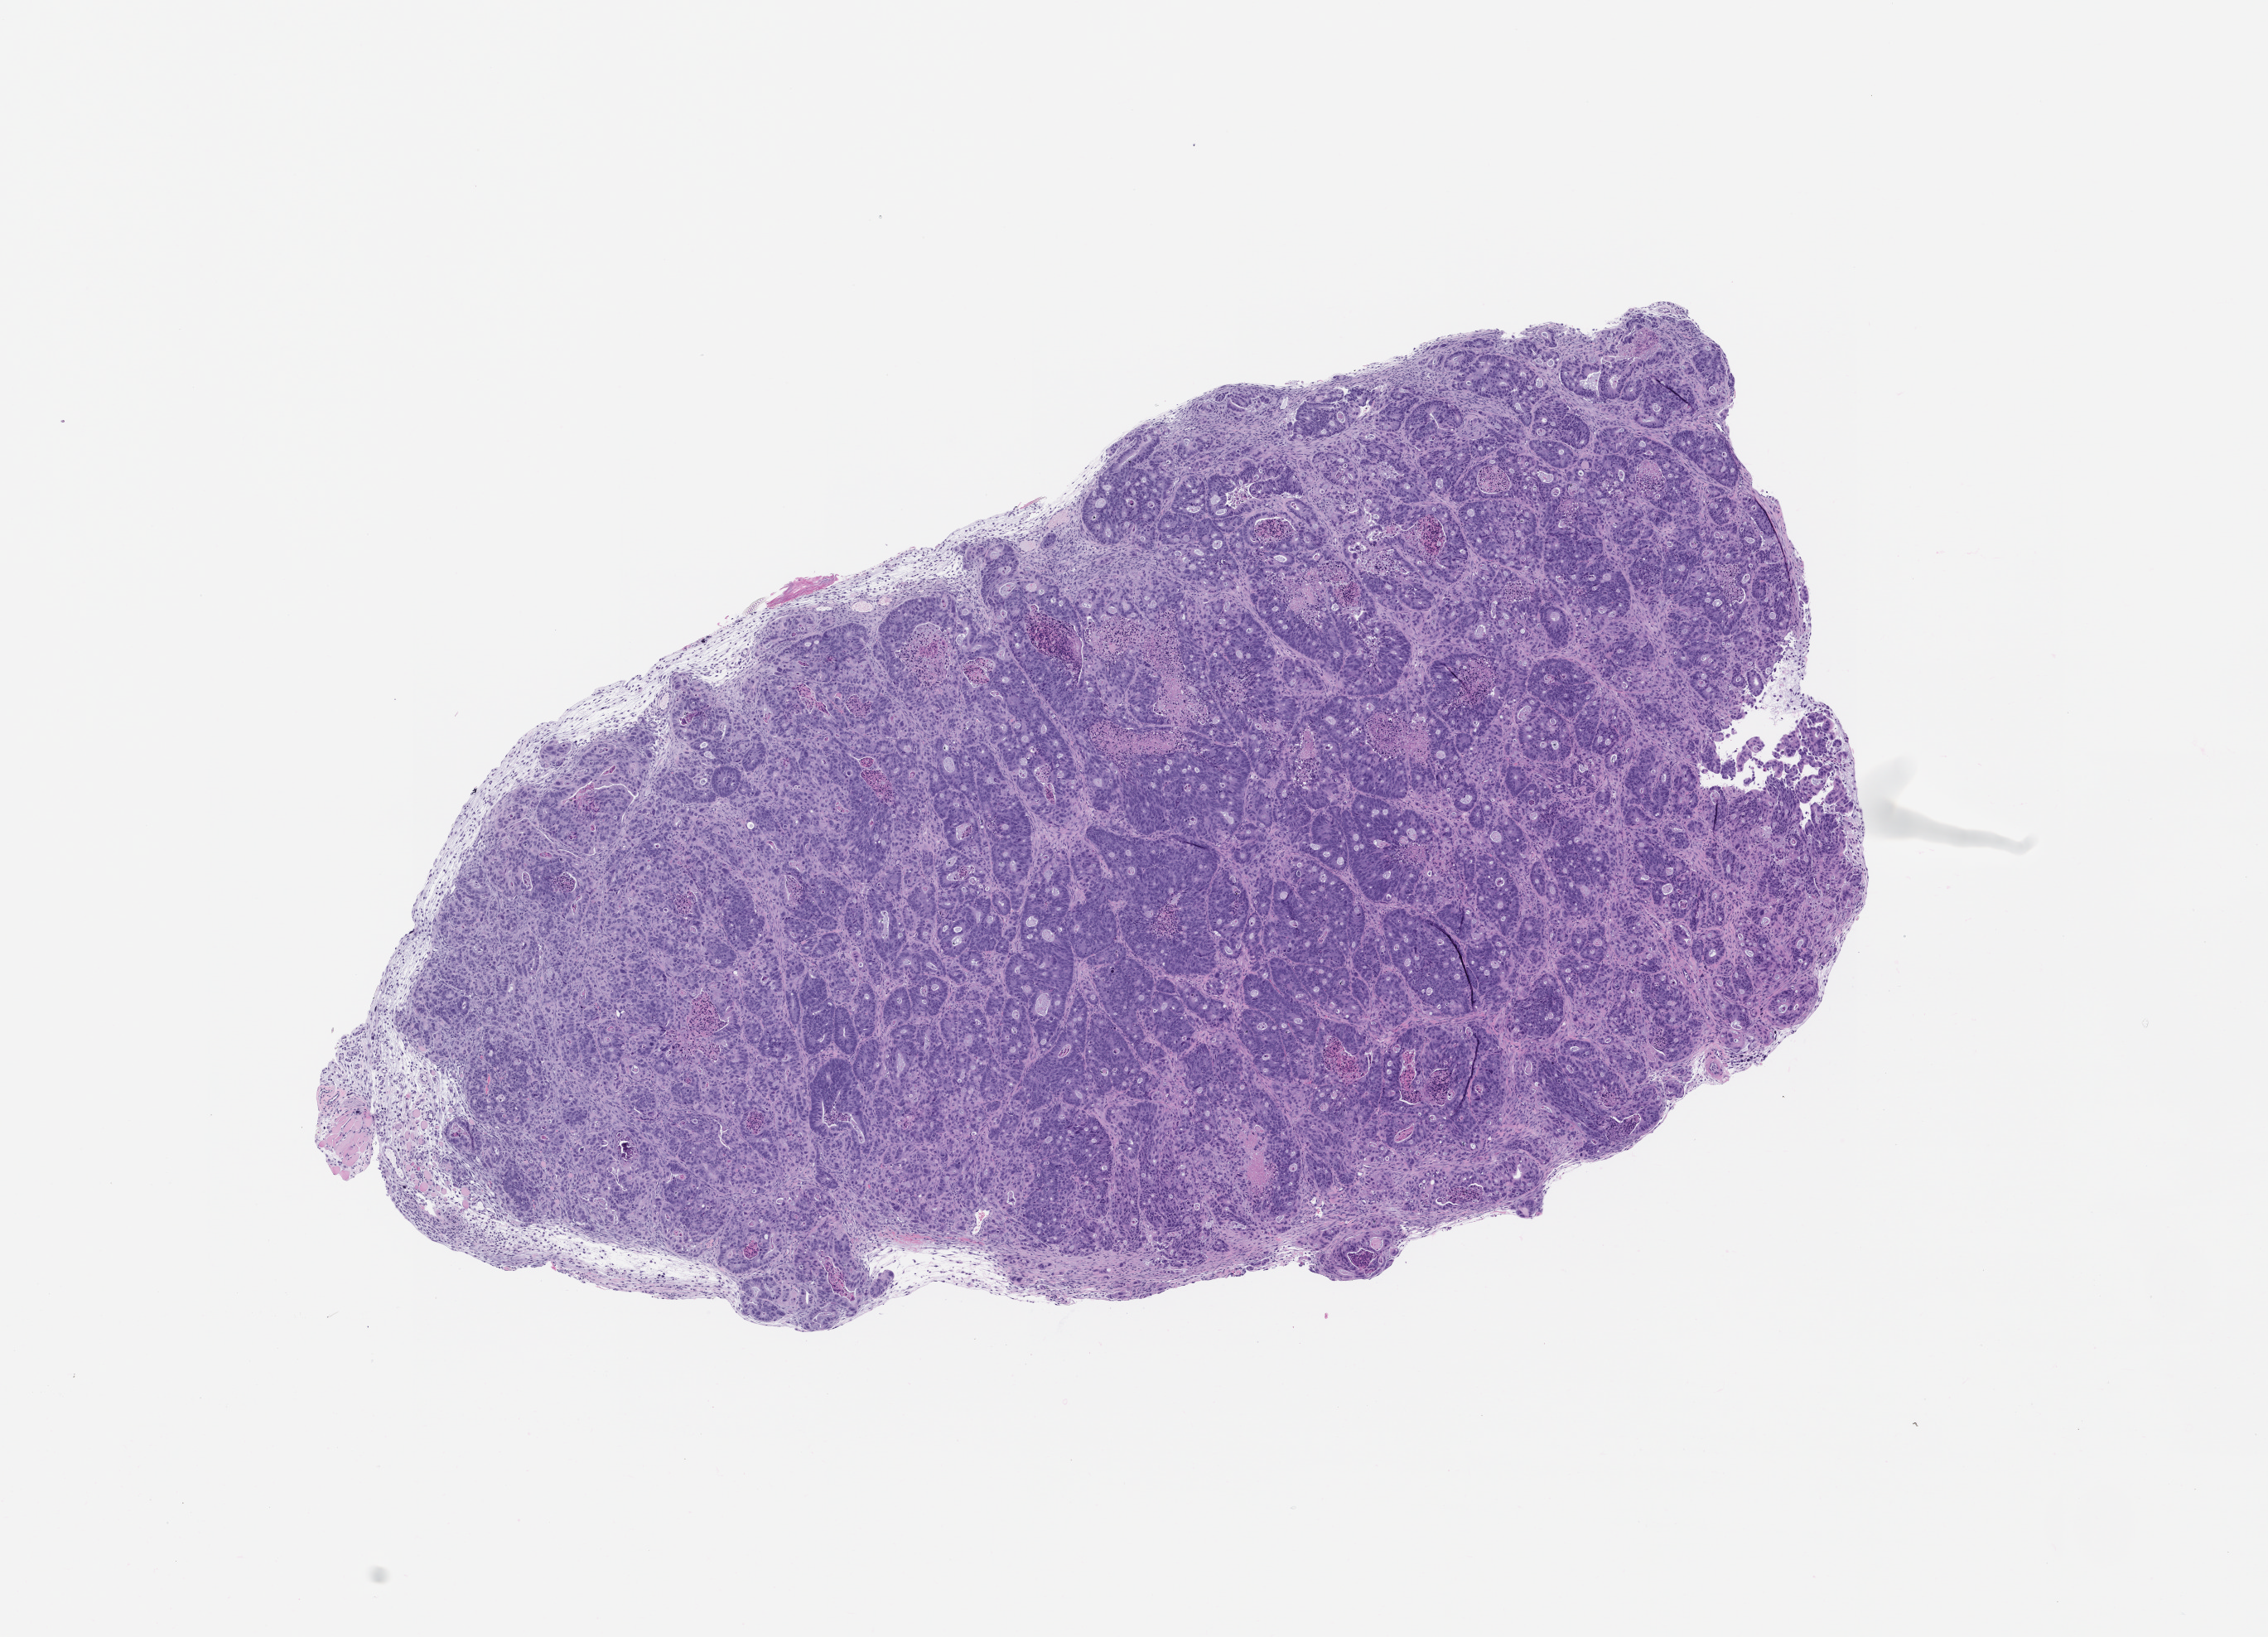
Whole-slide image, H&E: patient-derived xenograft (human tumor grown in a mouse), passage 3, low-resolution overview of the scanned area, about 11.0 x 7.9 mm; FFPE section; tumor site category: colon.
Originating patient diagnosis: Colon Adenocarcinoma.